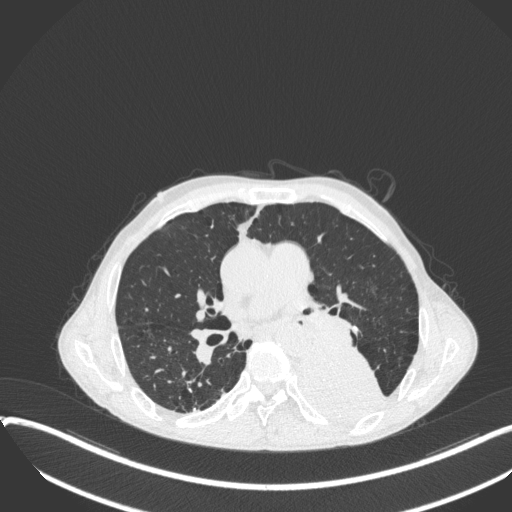
Chest CT, one axial slice. Position 206 of 400 along the scan axis. Reconstruction kernel B31f. 120 kVp. Lung window (W 1500 / L -600 HU). 1 mm slice thickness. 512 × 512 image matrix, field of view 400 × 400 mm. Male patient, age 57 years. Case-level facts recorded for this patient, not image findings: clinical TNM (as recorded): T4 N0 M0.
Structures marked on this image (bounding box drawn by a radiologist):
- lung tumour (recorded histology: squamous cell carcinoma): box from (x=292, y=338) to (x=383, y=423) px